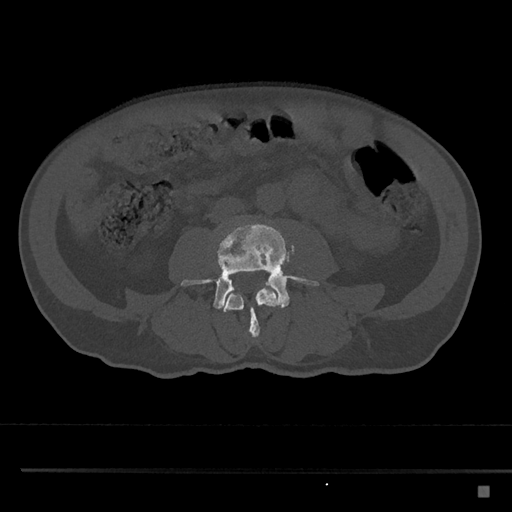
CT including the spine, one axial slice; reconstruction kernel Br40s/3; bone window (W 1800 / L 400 HU); 0.5 mm slice thickness; 512 × 512 image matrix. Patient: male, 59 years. From the clinical record (not read from this slice): primary cancer: prostate.
Structures marked on this image (semi-automatically segmented with operator editing):
- L3 vertebra: box from (x=222, y=284) to (x=282, y=337) px
- L4 vertebra: (x=181, y=222)–(x=319, y=309)